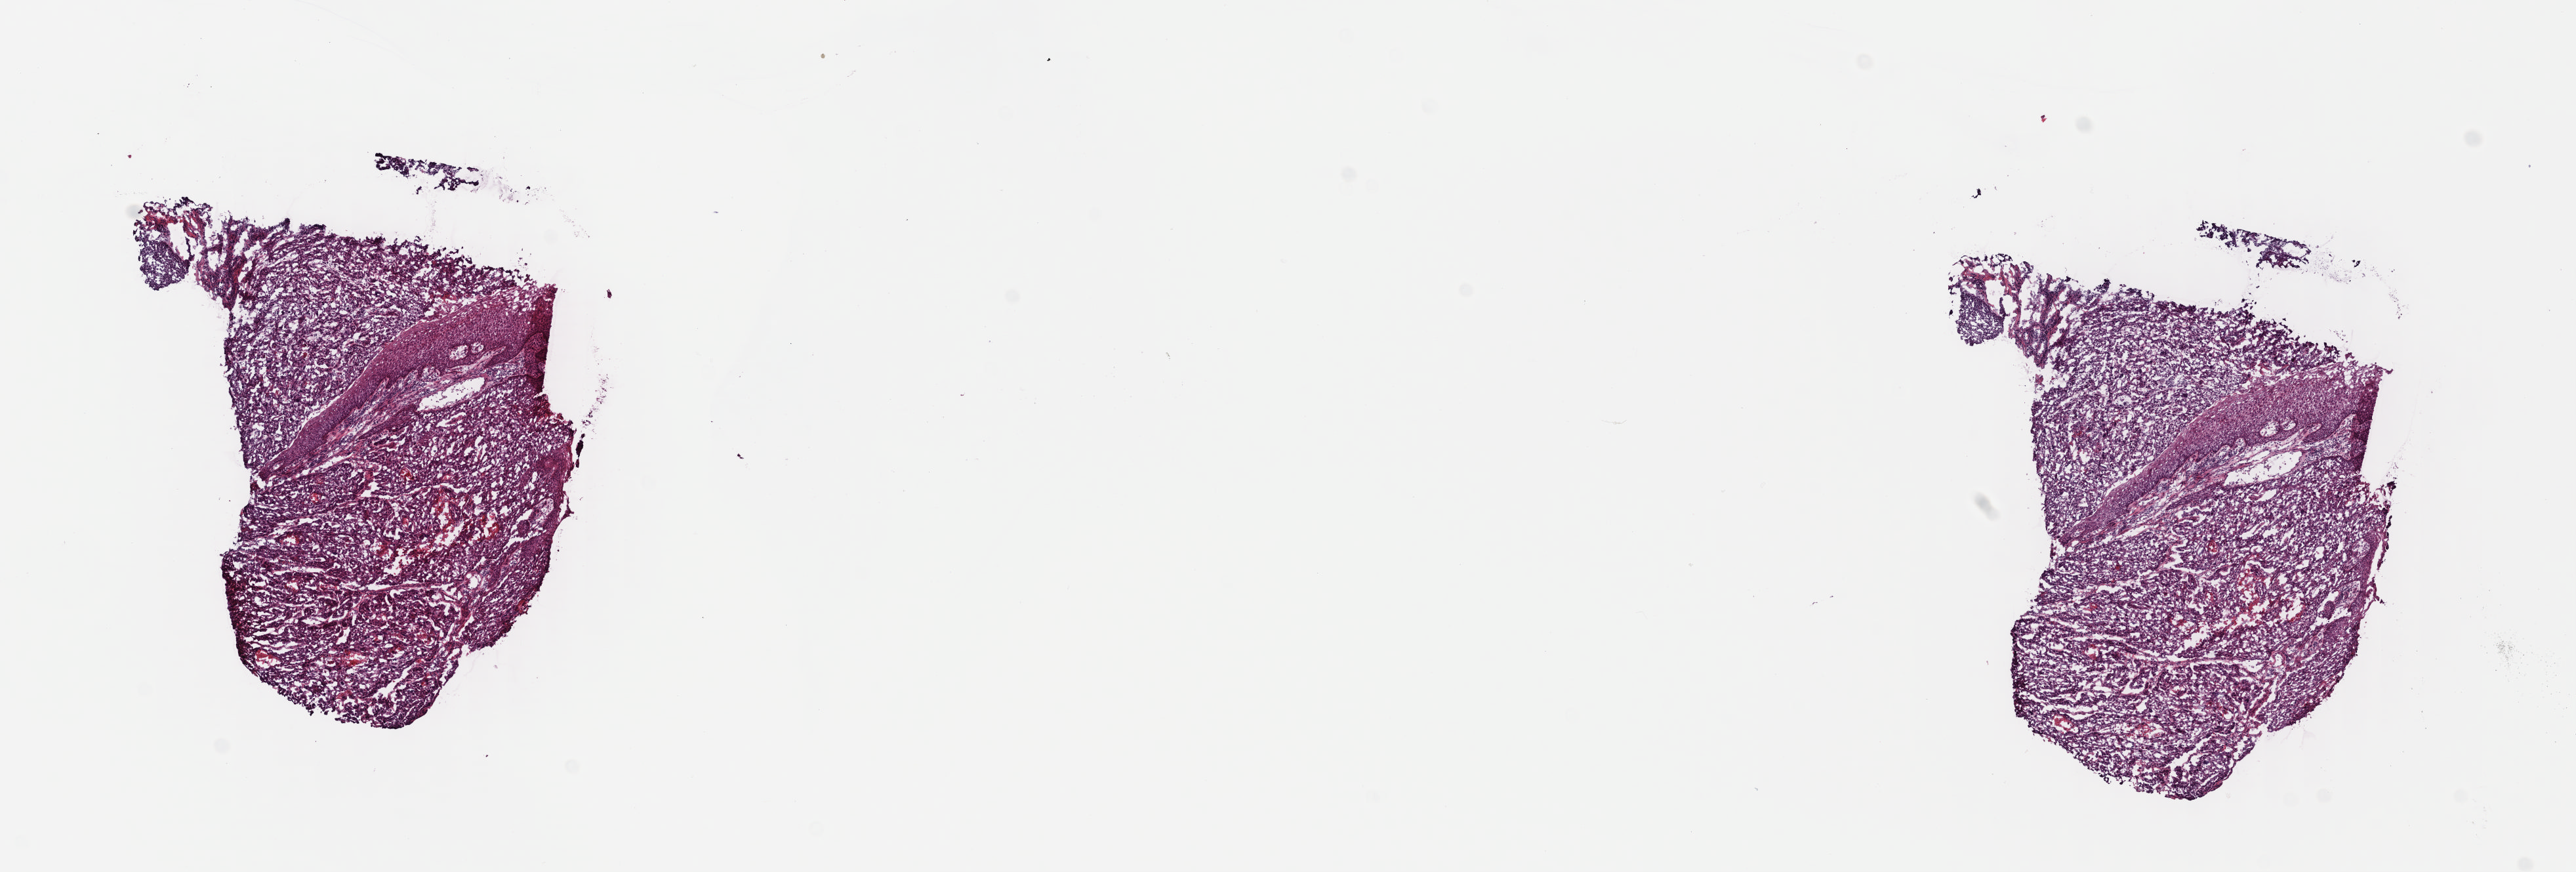
Whole-slide histology image, H&E — a low-resolution overview of the entire scanned area, about 15.4 x 5.2 mm; frozen section; sample: primary tumour, head and neck. Patient: male, age at initial diagnosis 50 years. Histologic grade: G3 (poorly differentiated). Composition of this section per pathologist review: tumour cells 80%, tumour nuclei 80%, normal cells 5%, stromal cells 10%, necrosis 5%. Infiltration values recorded for this section: lymphocyte infiltration 40%, monocyte infiltration 20%, neutrophil infiltration 20%.
- AJCC pathologic stage: IVA (7th edition)
- diagnosis: Squamous cell carcinoma, NOS (larynx, NOS)